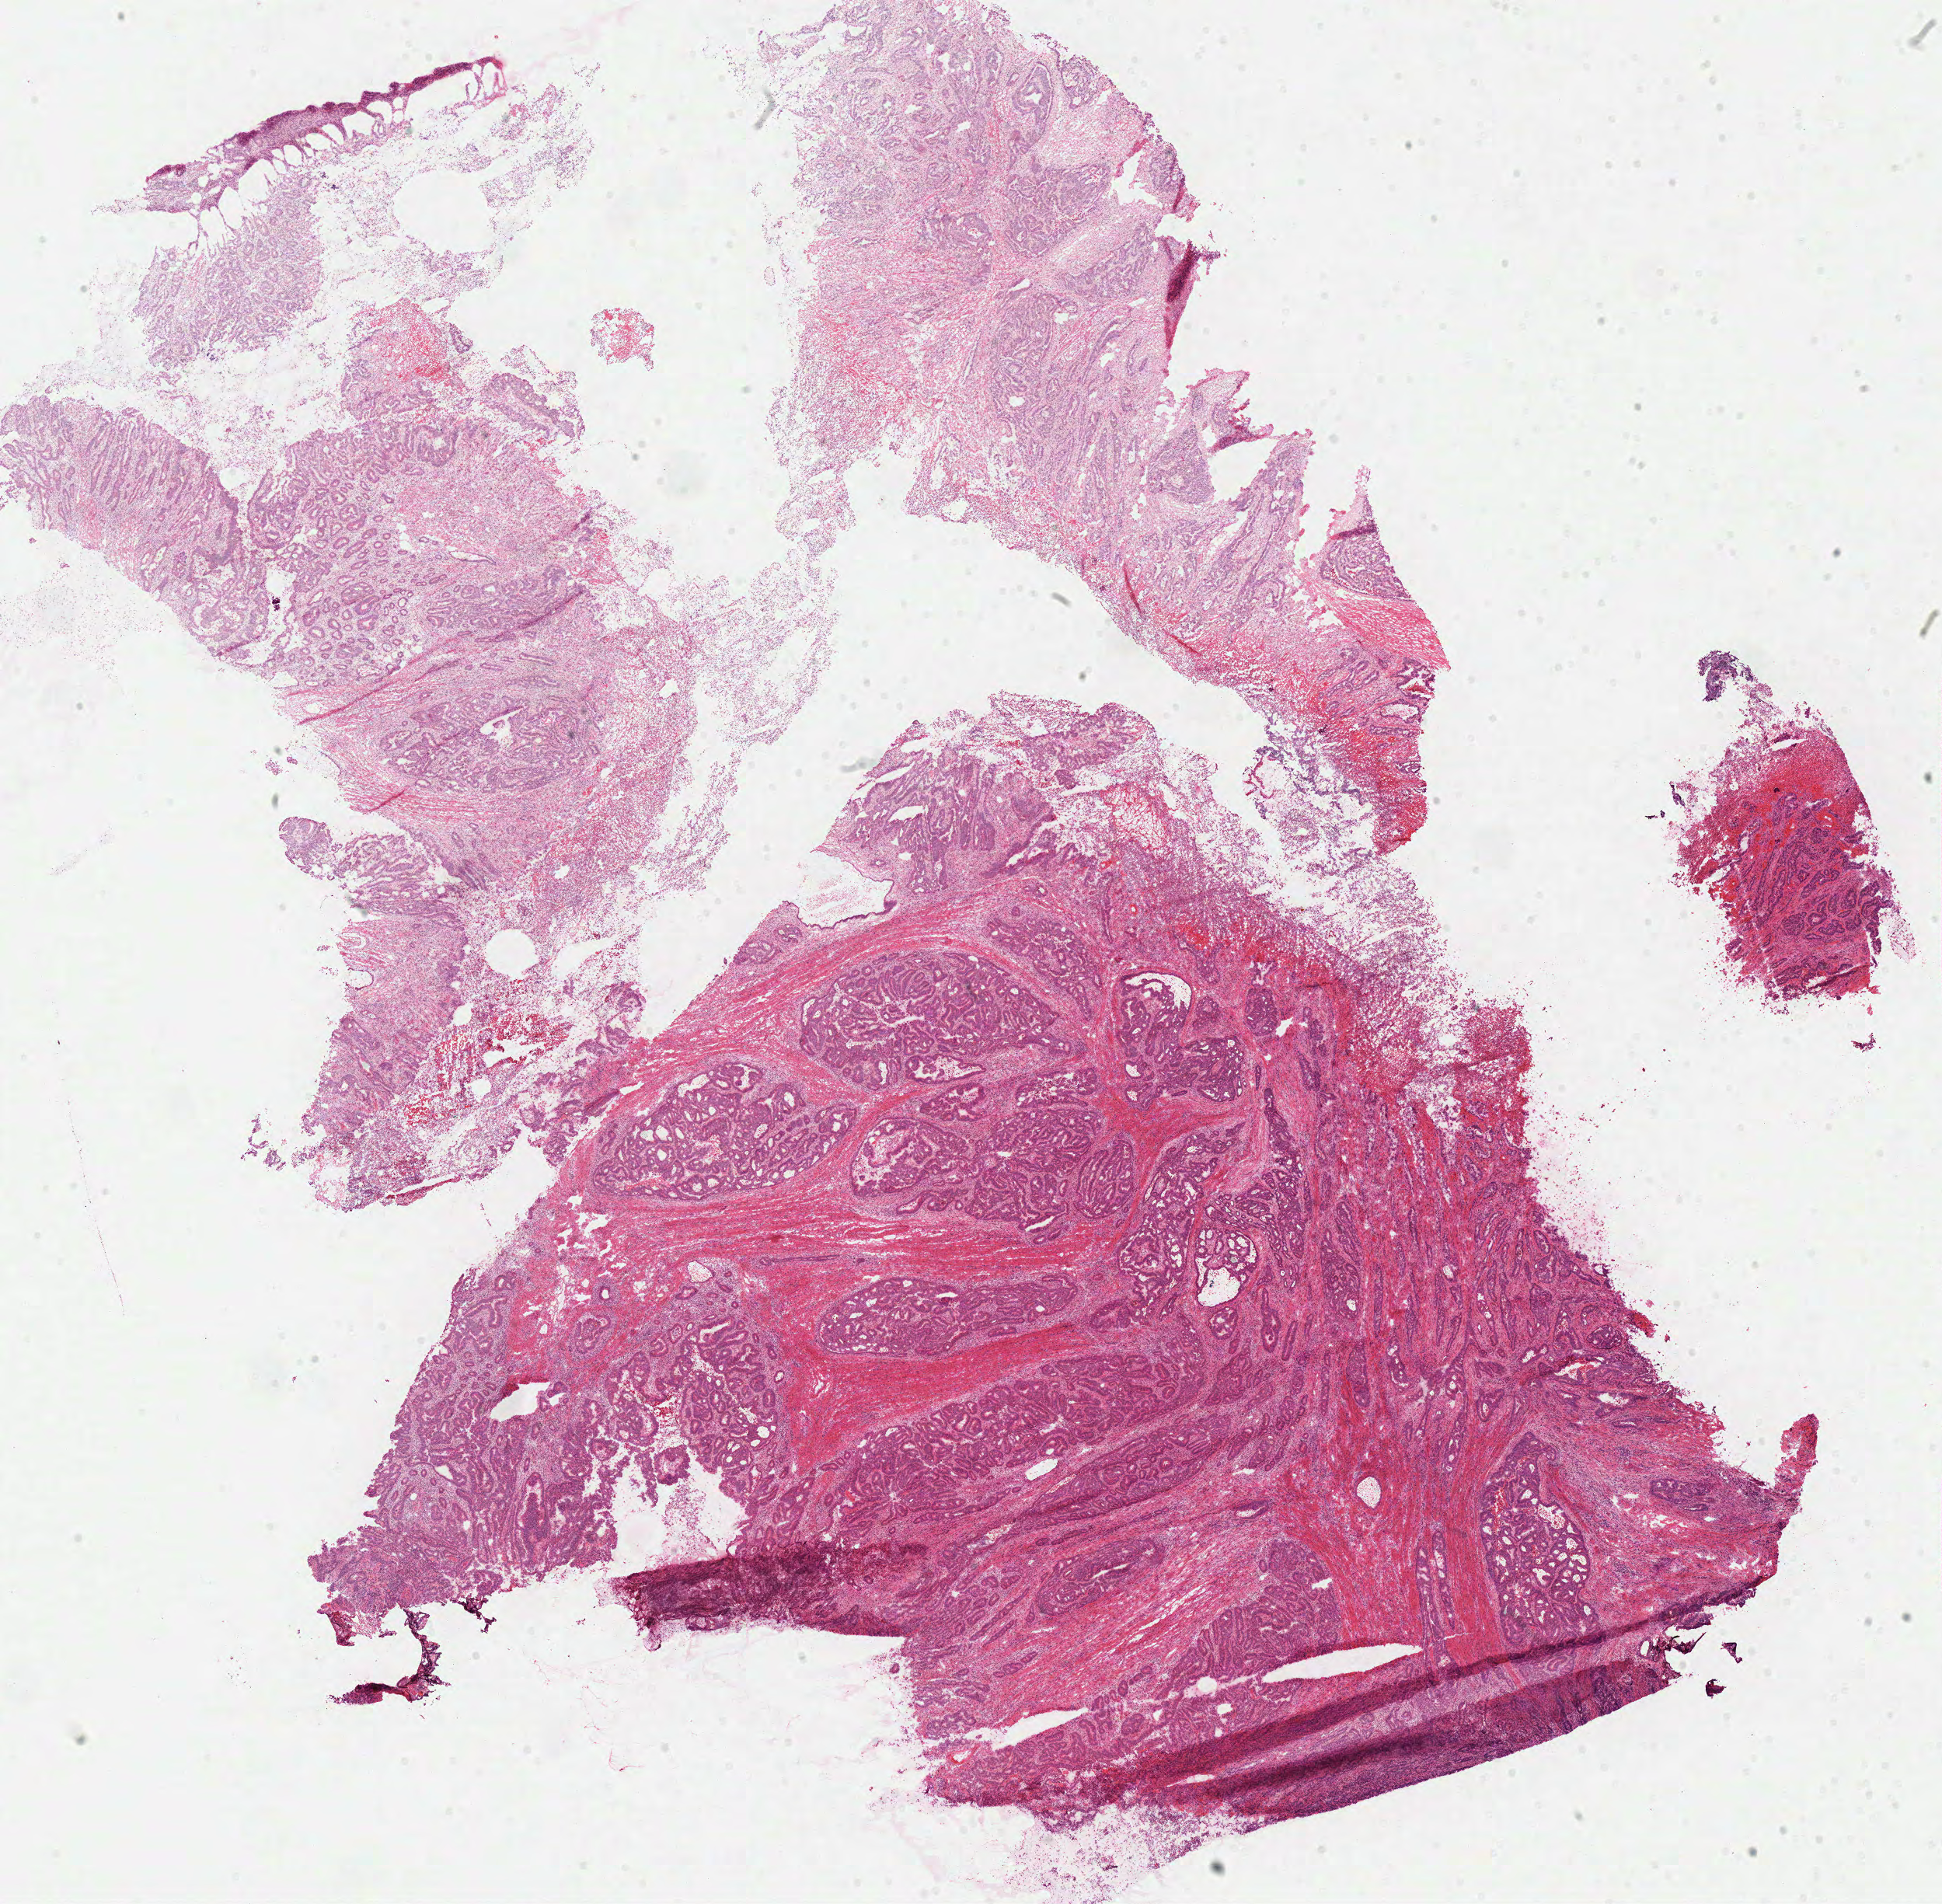
H&E-stained whole-slide image, shown as a low-resolution overview of the whole scanned area (about 19.7 x 19.3 mm, slide scanned at 40x); frozen section from the top of the tissue portion; primary tumour sample from the colon. Patient: female, age at initial diagnosis 46 years. Pathologist review of this section (percent, as recorded): tumour cells 78%, tumour nuclei 80%, normal cells 2%, stromal cells 15%, necrosis 5%.
• AJCC pathologic stage: IIA
• histologic diagnosis: Adenocarcinoma, NOS (sigmoid colon)